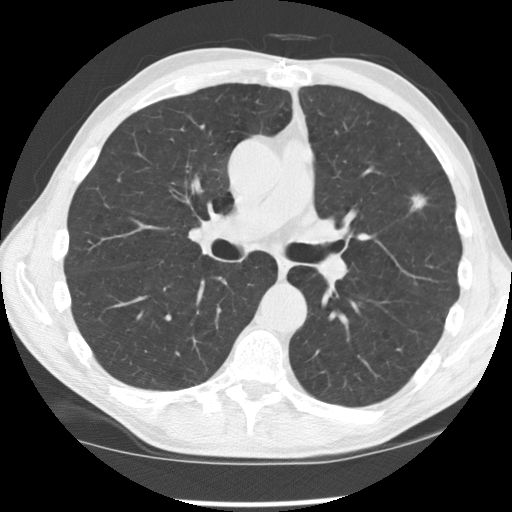
Low-dose screening chest CT, axial slice, second screening round (one year after baseline), lung window (W 1500 / L -600 HU), 2.5 mm slice thickness, standard (soft-tissue) reconstruction kernel (STANDARD), 512 × 512 image matrix. Male participant, aged 64 years at enrolment. Current smoker at enrolment.
- Expert reader's lesion annotation, bounding box [x1, y1, x2, y2] px = [389, 179, 444, 224].
- Reader record for this screening exam (exam-level; its link to the box is not recorded): non-calcified nodule or mass ≥4 mm, left upper lobe, 16 × 11 mm, spiculated (stellate) margins, soft tissue attenuation, pre-existing on the prior screen: yes; interval growth: yes.
- Lung cancer was diagnosed 59 days after this screen: adenocarcinoma, NOS, left upper lobe, poorly differentiated (G3), stage IA (AJCC 6th edition), 10 mm at pathology.